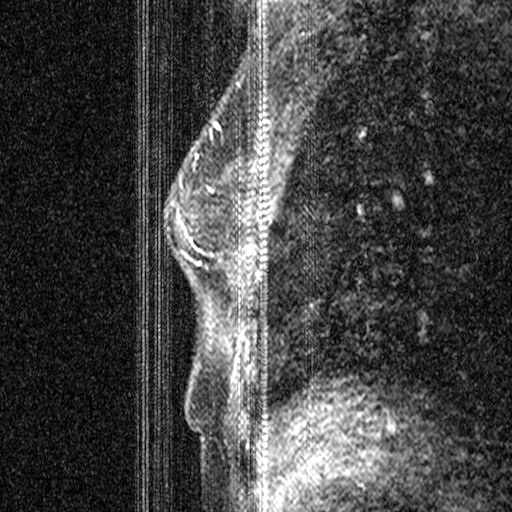
Breast MRI (dynamic contrast-enhanced), one sagittal slice; position 20 of 44 along the scan axis; dynamic contrast-enhanced study with each time point stored as its own series, time point 2 of 3 at this slice position (early post-contrast, ordered by acquisition time); 1.5 T; TE 4.5 ms, TR 11 ms; 3 mm slice thickness; 512 × 512 image matrix, field of view 200 × 200 mm. Patient: female, 44 years. From the clinical record (not read from this slice): setting: breast cancer imaged before/during neoadjuvant chemotherapy; receptor status: HR-positive, HER2-negative.
Outlined on this slice (semi-automatically segmented with operator editing):
- analysis volume of interest (the breast-tissue region the enhancement analysis was run in; not a lesion): bounding box [x1, y1, x2, y2] px = [206, 164, 238, 299]
- tumour enhancement mask (voxels above the 90 % enhancement threshold inside the analysis volume of interest): [209, 253, 212, 255]